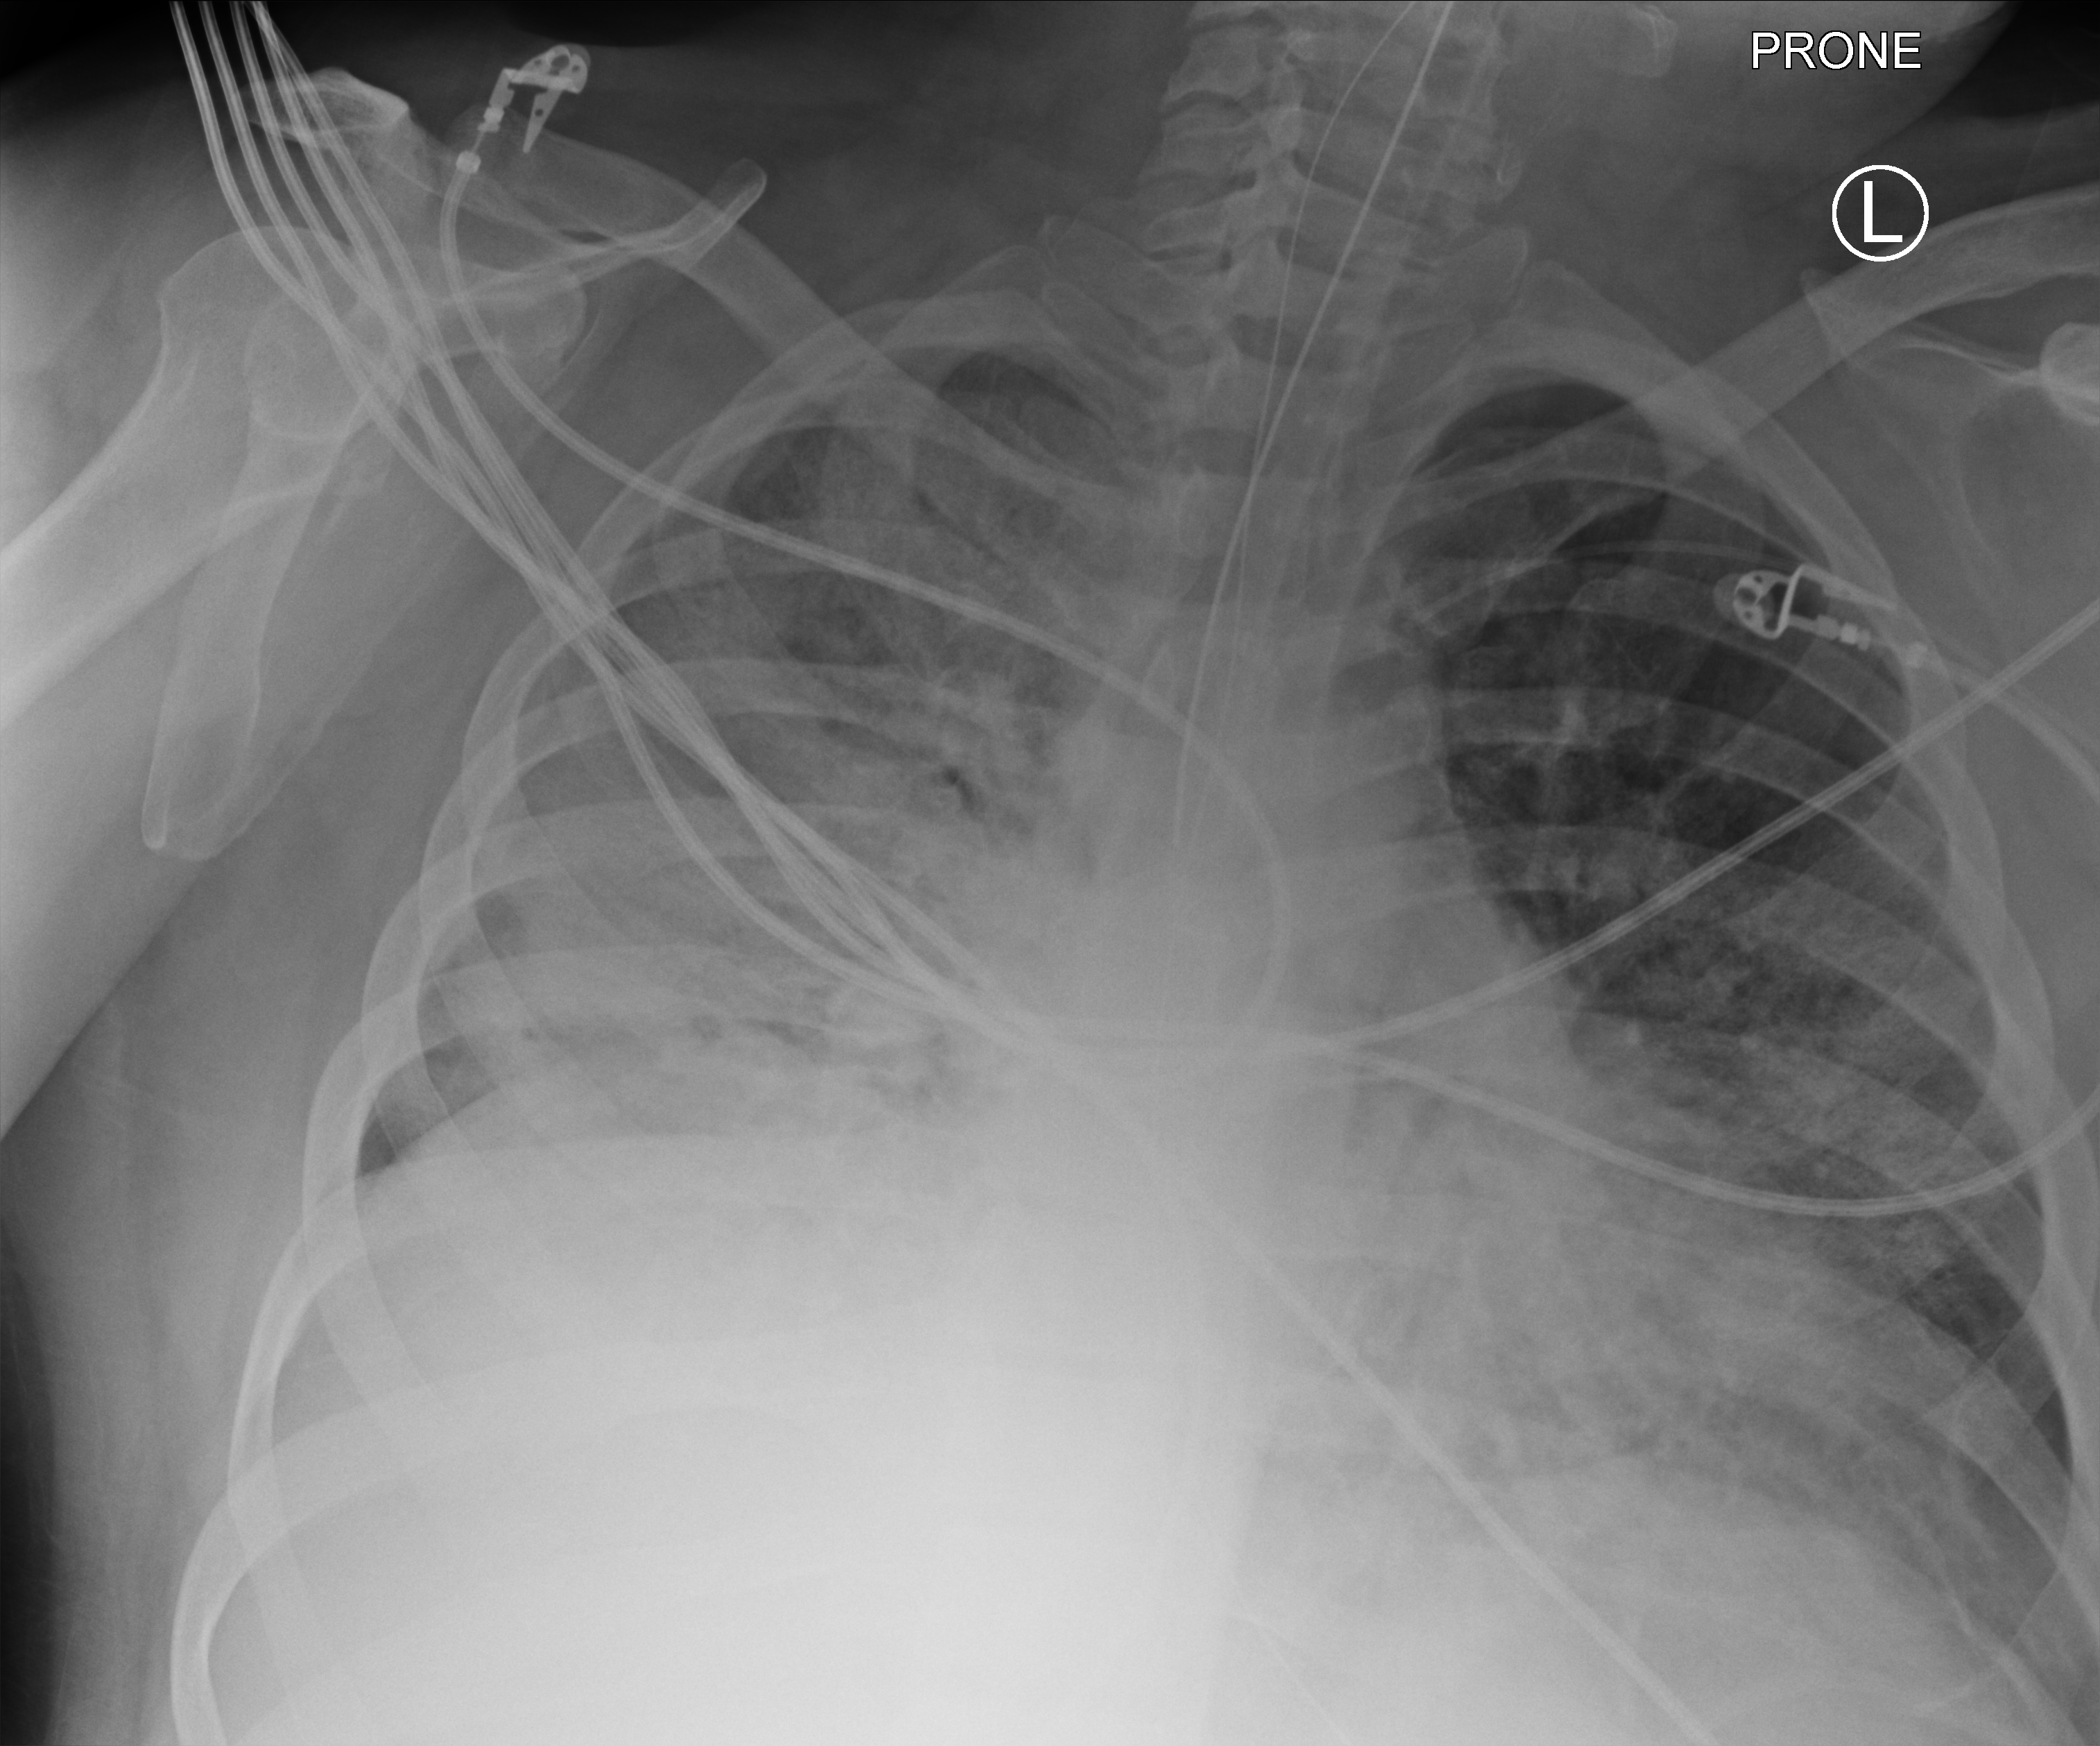
Portable chest radiograph; anteroposterior (AP) projection. Male patient hospitalised with COVID-19, age 18–59 years.
From the hospital-stay record, not from the radiograph (when in the stay this image was taken is not recorded): smoking status (admission record): never; admitted to intensive care during this hospital stay: yes.